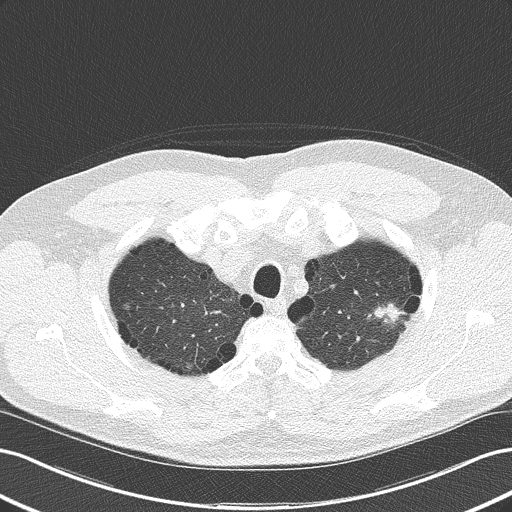
Low-dose screening chest CT, axial slice. Second annual screen. Lung window (W 1500 / L -600 HU). 2 mm slice thickness. 512 × 512 image matrix. Male, age 62 years at enrolment. Current smoker at enrolment.
- Expert reader's lesion annotation, bounding box <356,287,417,339> (left, top, right, bottom; pixels).
- The screening reader recorded 2 non-calcified nodules or masses ≥4 mm on this exam (left upper lobe, right middle lobe); which of them this box marks is not recorded.
- Official screen result: positive, other.